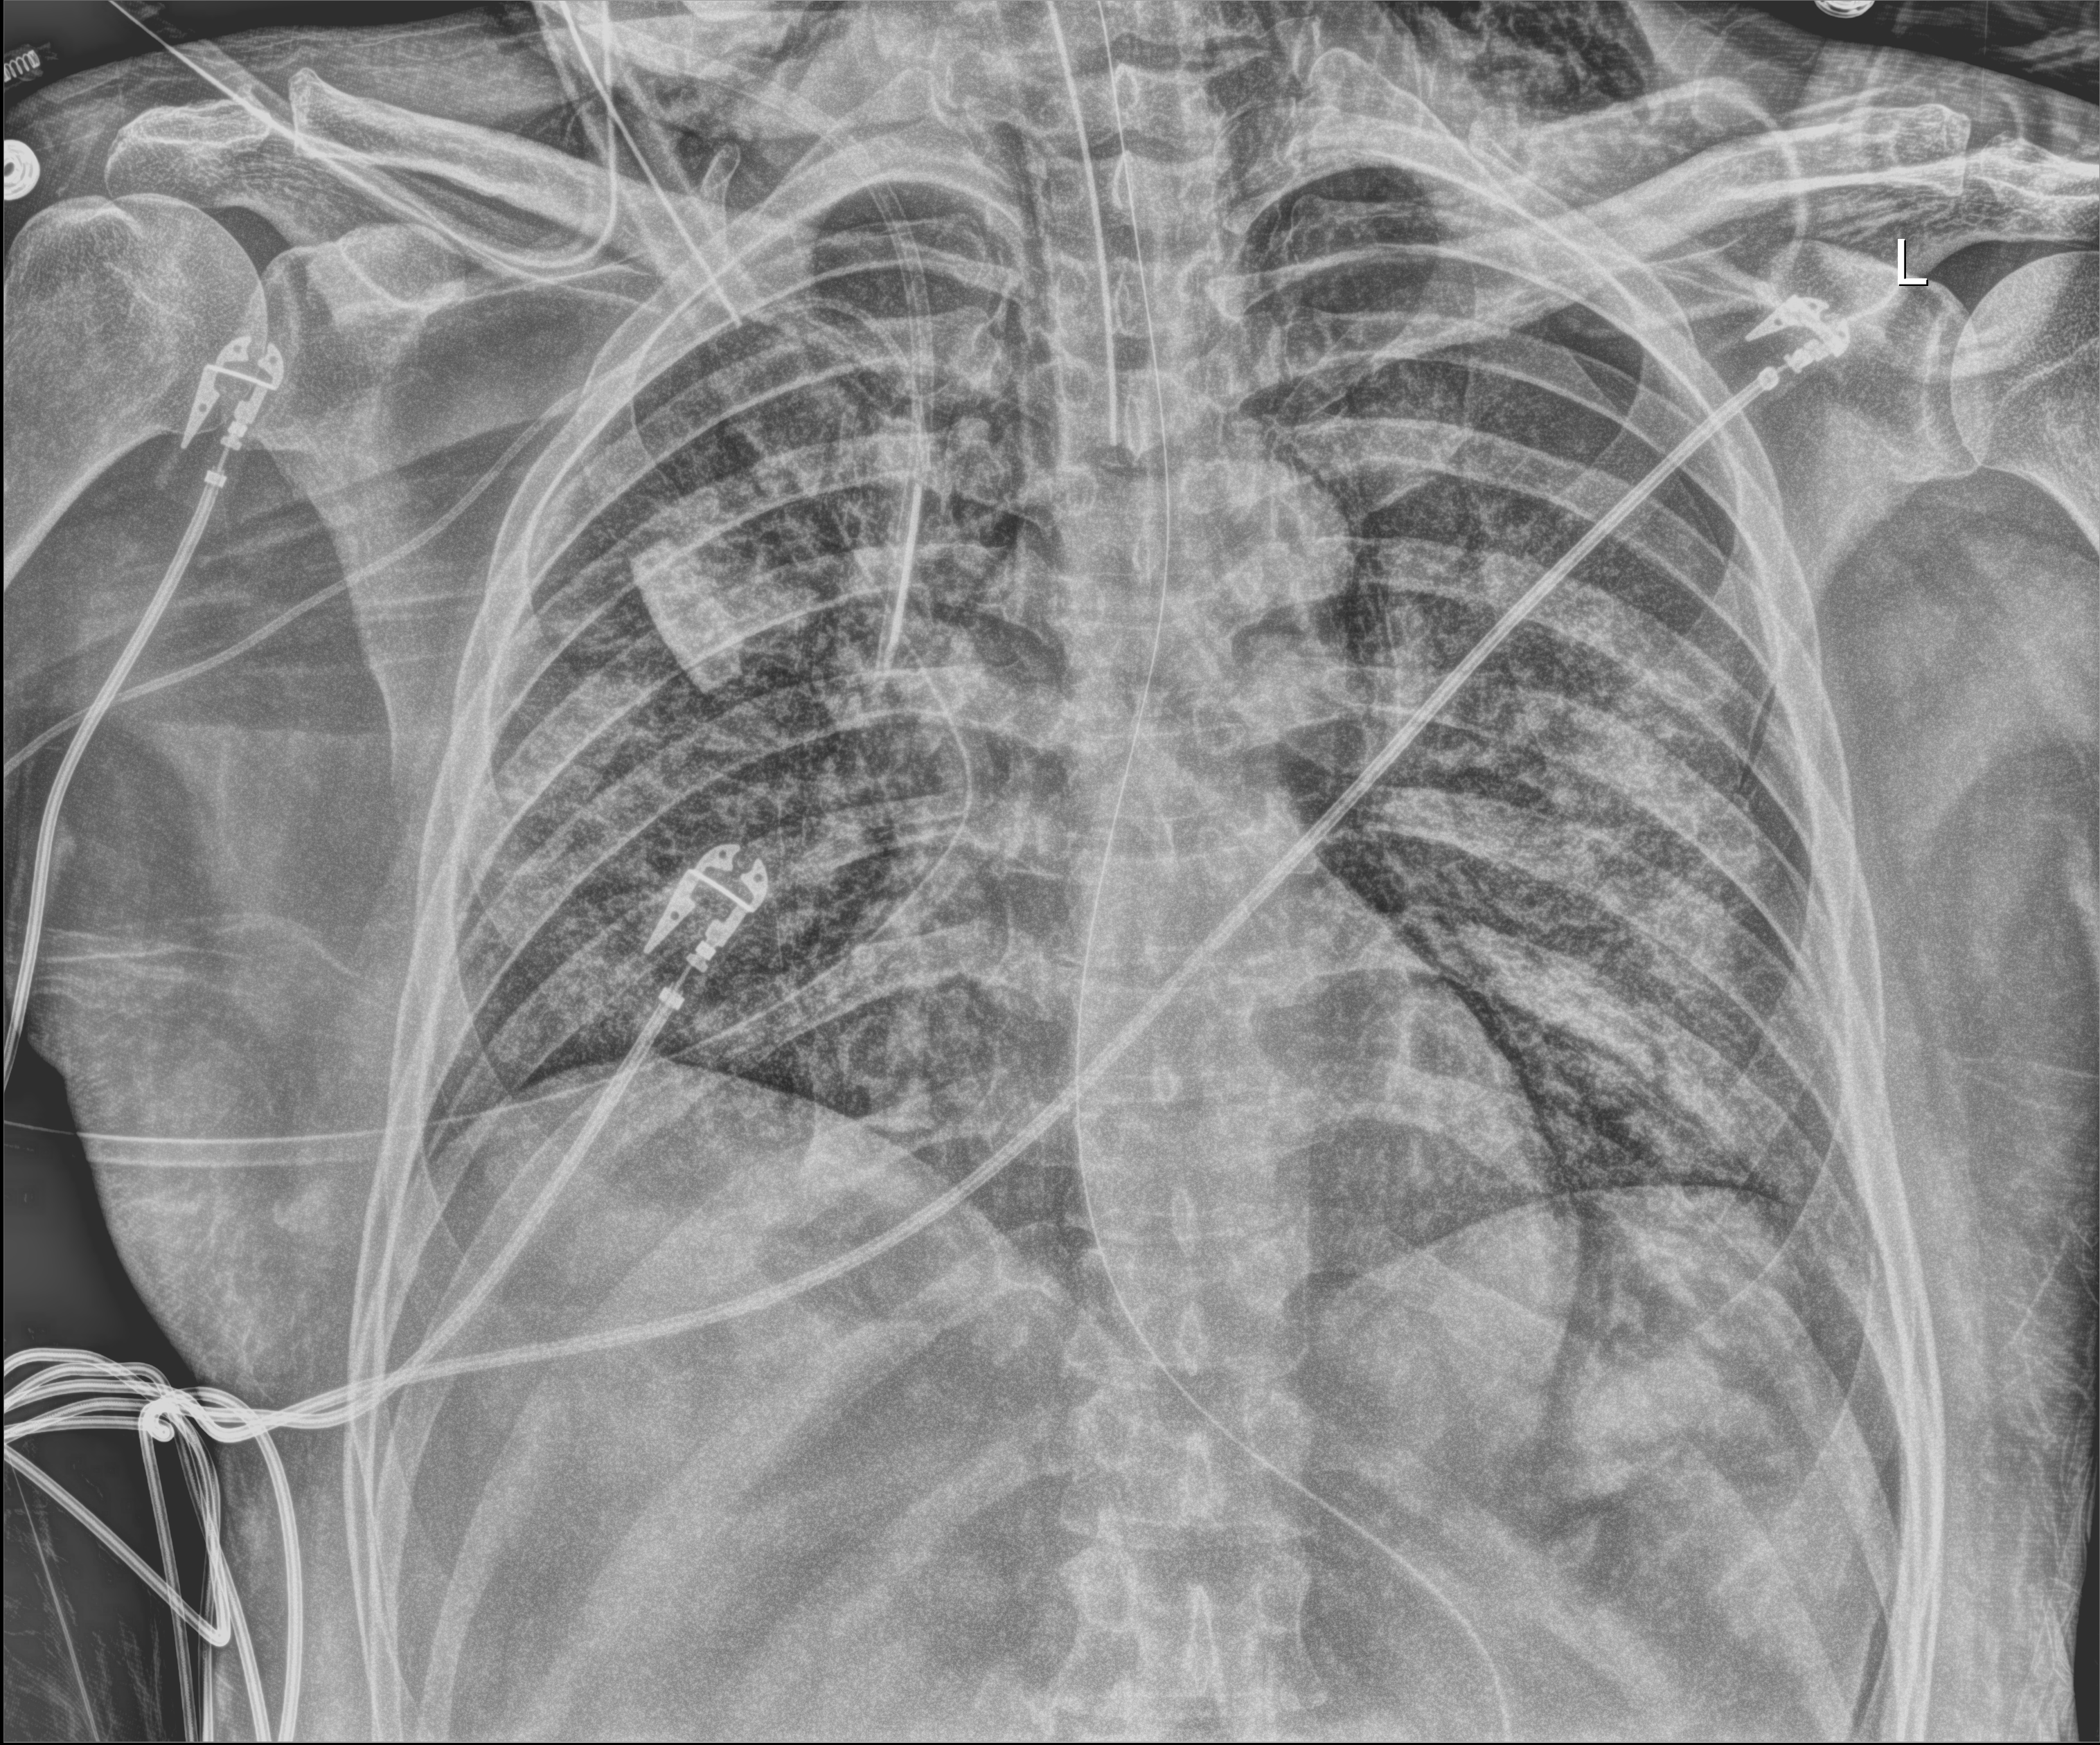
Bedside chest radiograph (digital radiography); anteroposterior (AP) projection. Patient hospitalised with COVID-19; male, aged 18–59 years.
From the hospital-stay record, not from the radiograph (when in the stay this image was taken is not recorded): chronic kidney disease (admission record): no; admitted to intensive care during this hospital stay: yes; length of hospital stay: 77 days.